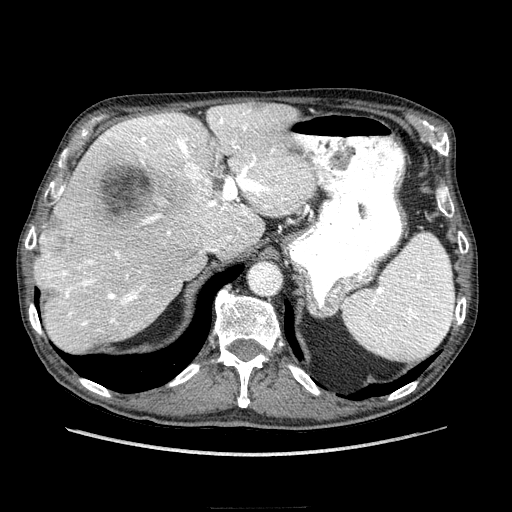
Contrast-enhanced abdominal CT (liver protocol), one axial slice. Reconstruction kernel STANDARD. Soft-tissue window (W 400 / L 40 HU). 512 × 512 image matrix. Case-level facts recorded for this patient, not image findings: diagnosis: hepatocellular carcinoma (patient treated with transarterial chemoembolisation; whether this scan precedes or follows treatment is not stated here); TNM stage (as recorded): Stage-IIIA; Child-Pugh class: A; tumour nodularity: multinodular; tumour size: 20 cm.
Structures marked on this image (semi-automatically segmented with operator editing):
- abdominal aorta: bounding box <251,262,280,295> (left, top, right, bottom; pixels)
- liver parenchyma outside the tumour (the mass and vessels are separate outlines, so this box may not span the whole liver): <35,104,308,352>
- mass: <56,160,192,251>
- liver vessels: <42,108,306,332>